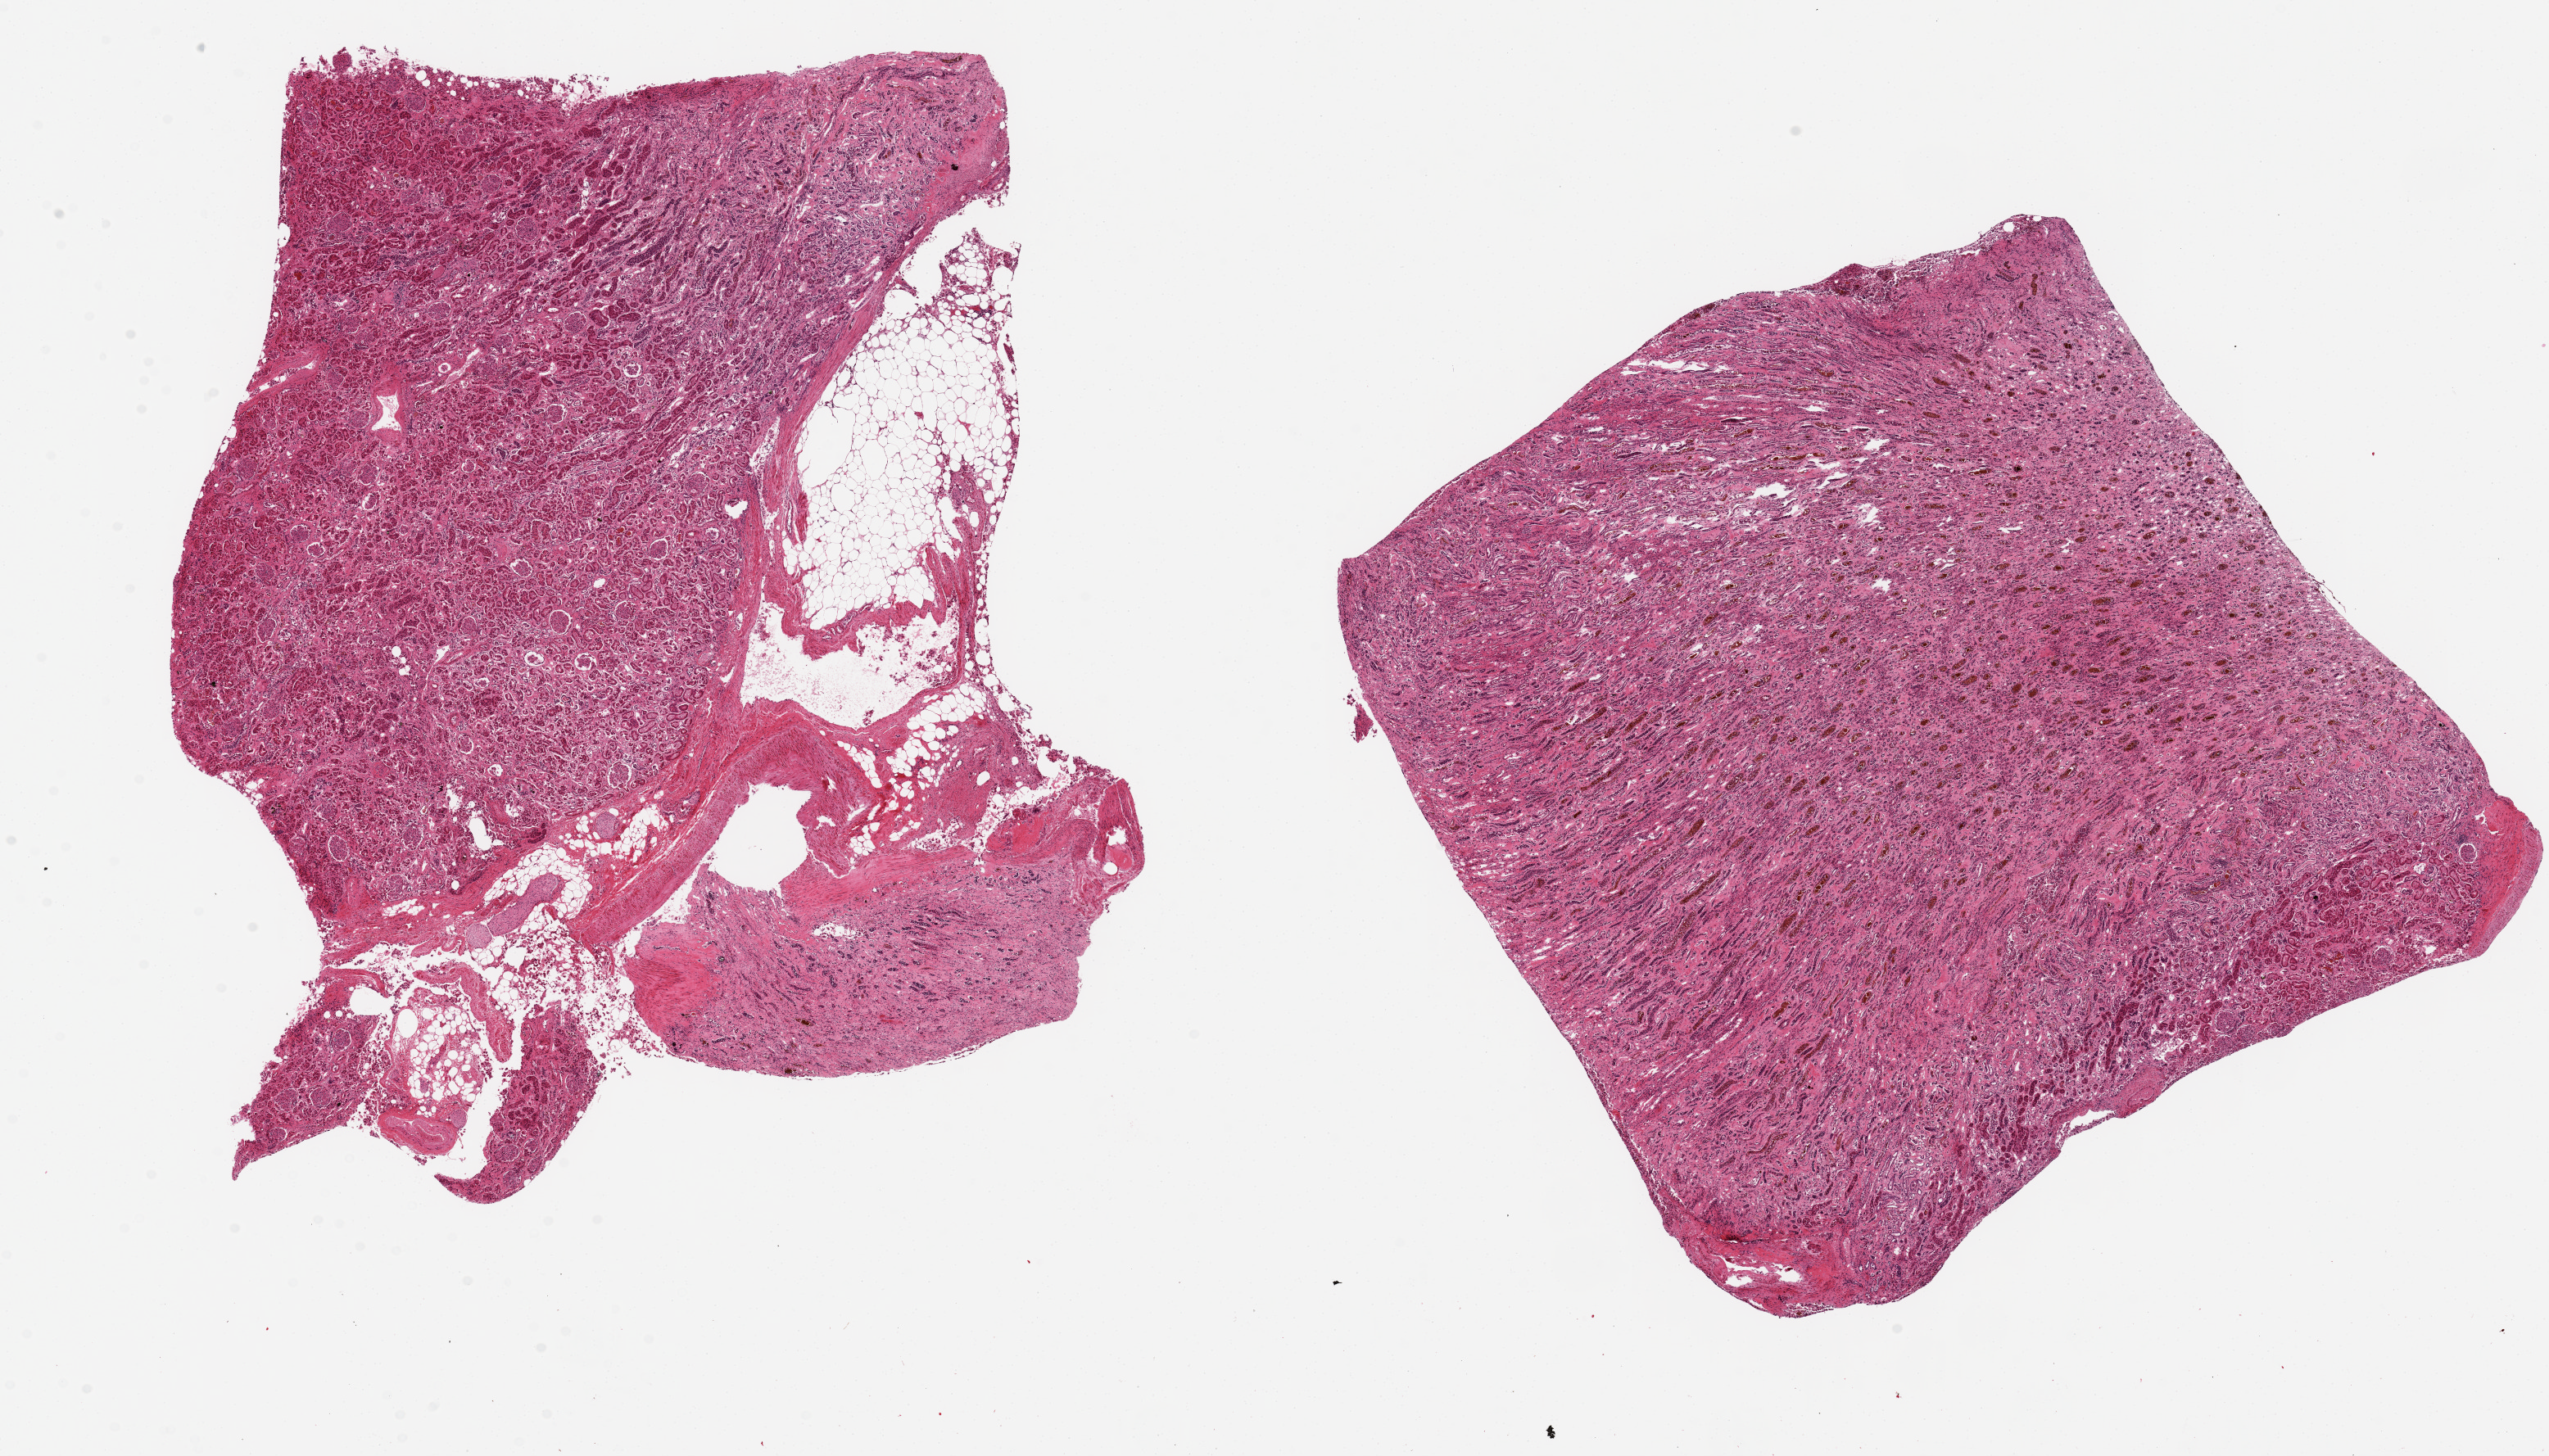
Digitized haematoxylin and eosin-stained section — low-resolution overview of the scanned area, about 24.6 x 14.1 mm (slide scanned at 20x); PAXgene-fixed, paraffin-embedded tissue; sampled site (target tissue): renal medulla; donor tissue sample. Donor: male.
Review note (as recorded): 2 ~9x8mm aliquots. One medulla, one cortex, tubules badly autolyzed.